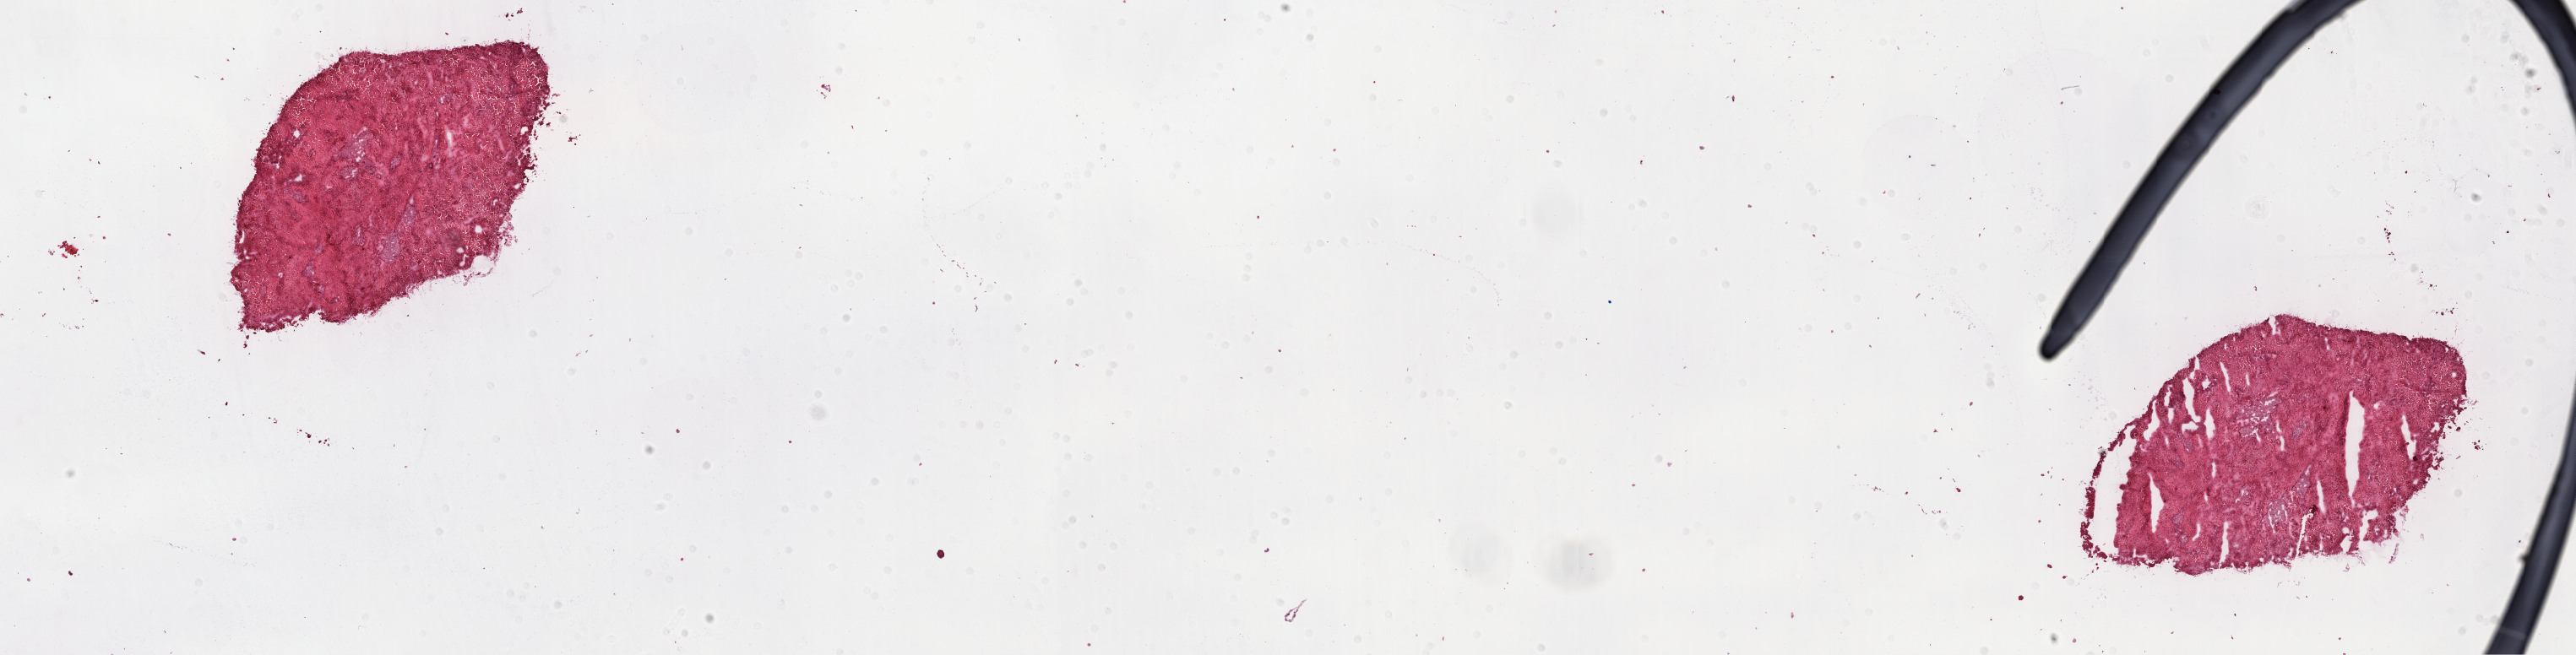
Hematoxylin and eosin (H&E) stained whole-slide image — a low-resolution overview of the entire scanned area, about 24.7 x 6.3 mm (acquisition: 40x scan). Frozen section from the top of the tissue portion. Primary tumour sample from the kidney. Patient: male, age at initial diagnosis 64 years. Pathologist review of this section (percent, as recorded): tumour cells 81%, tumour nuclei 70%.
Histologic diagnosis: Papillary adenocarcinoma, NOS.